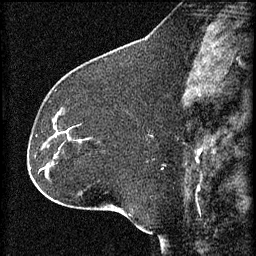
Breast MRI (dynamic contrast-enhanced), one sagittal slice. Slice 26 of 60 in the series (ordered by position). 3 images stored at this slice position (order not interpretable as contrast timing). 1.5 T. TE 4.2 ms, TR 8.2 ms. 2 mm slice thickness. 256 × 256 image matrix. Patient: female, 32 years.
Outlined on this slice (semi-automatically segmented with operator editing):
- analysis volume of interest (the breast-tissue region the enhancement analysis was run in; not a lesion): bounding box <47,114,84,157> (left, top, right, bottom; pixels)
- tumour enhancement mask (voxels above the 70 % enhancement threshold inside the analysis volume of interest): <56,130,69,135>